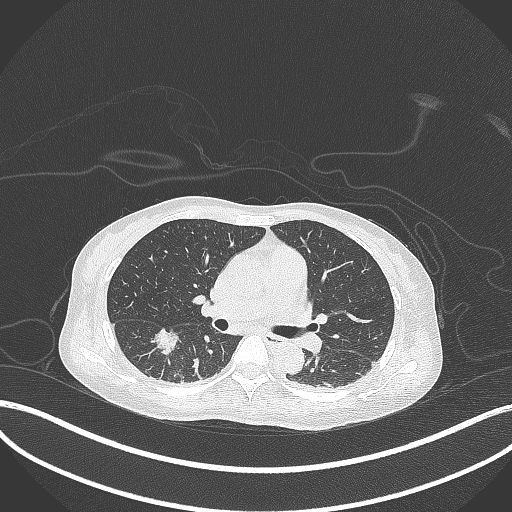
Chest CT, one axial slice; slice 176 of 261 in the series (ordered by position); reconstruction kernel B70f; 120 kVp; lung window (W 1500 / L -600 HU); 1 mm slice thickness; 512 × 512 image matrix, field of view 400 × 400 mm. Female patient, age 44 years. Case-level facts recorded for this patient, not image findings: clinical TNM (as recorded): T1c N0 M0.
Structures marked on this image (bounding box drawn by a radiologist):
- lung tumour (recorded histology: adenocarcinoma): bounding box (x1, y1, x2, y2) in pixels: (151, 325, 180, 353)